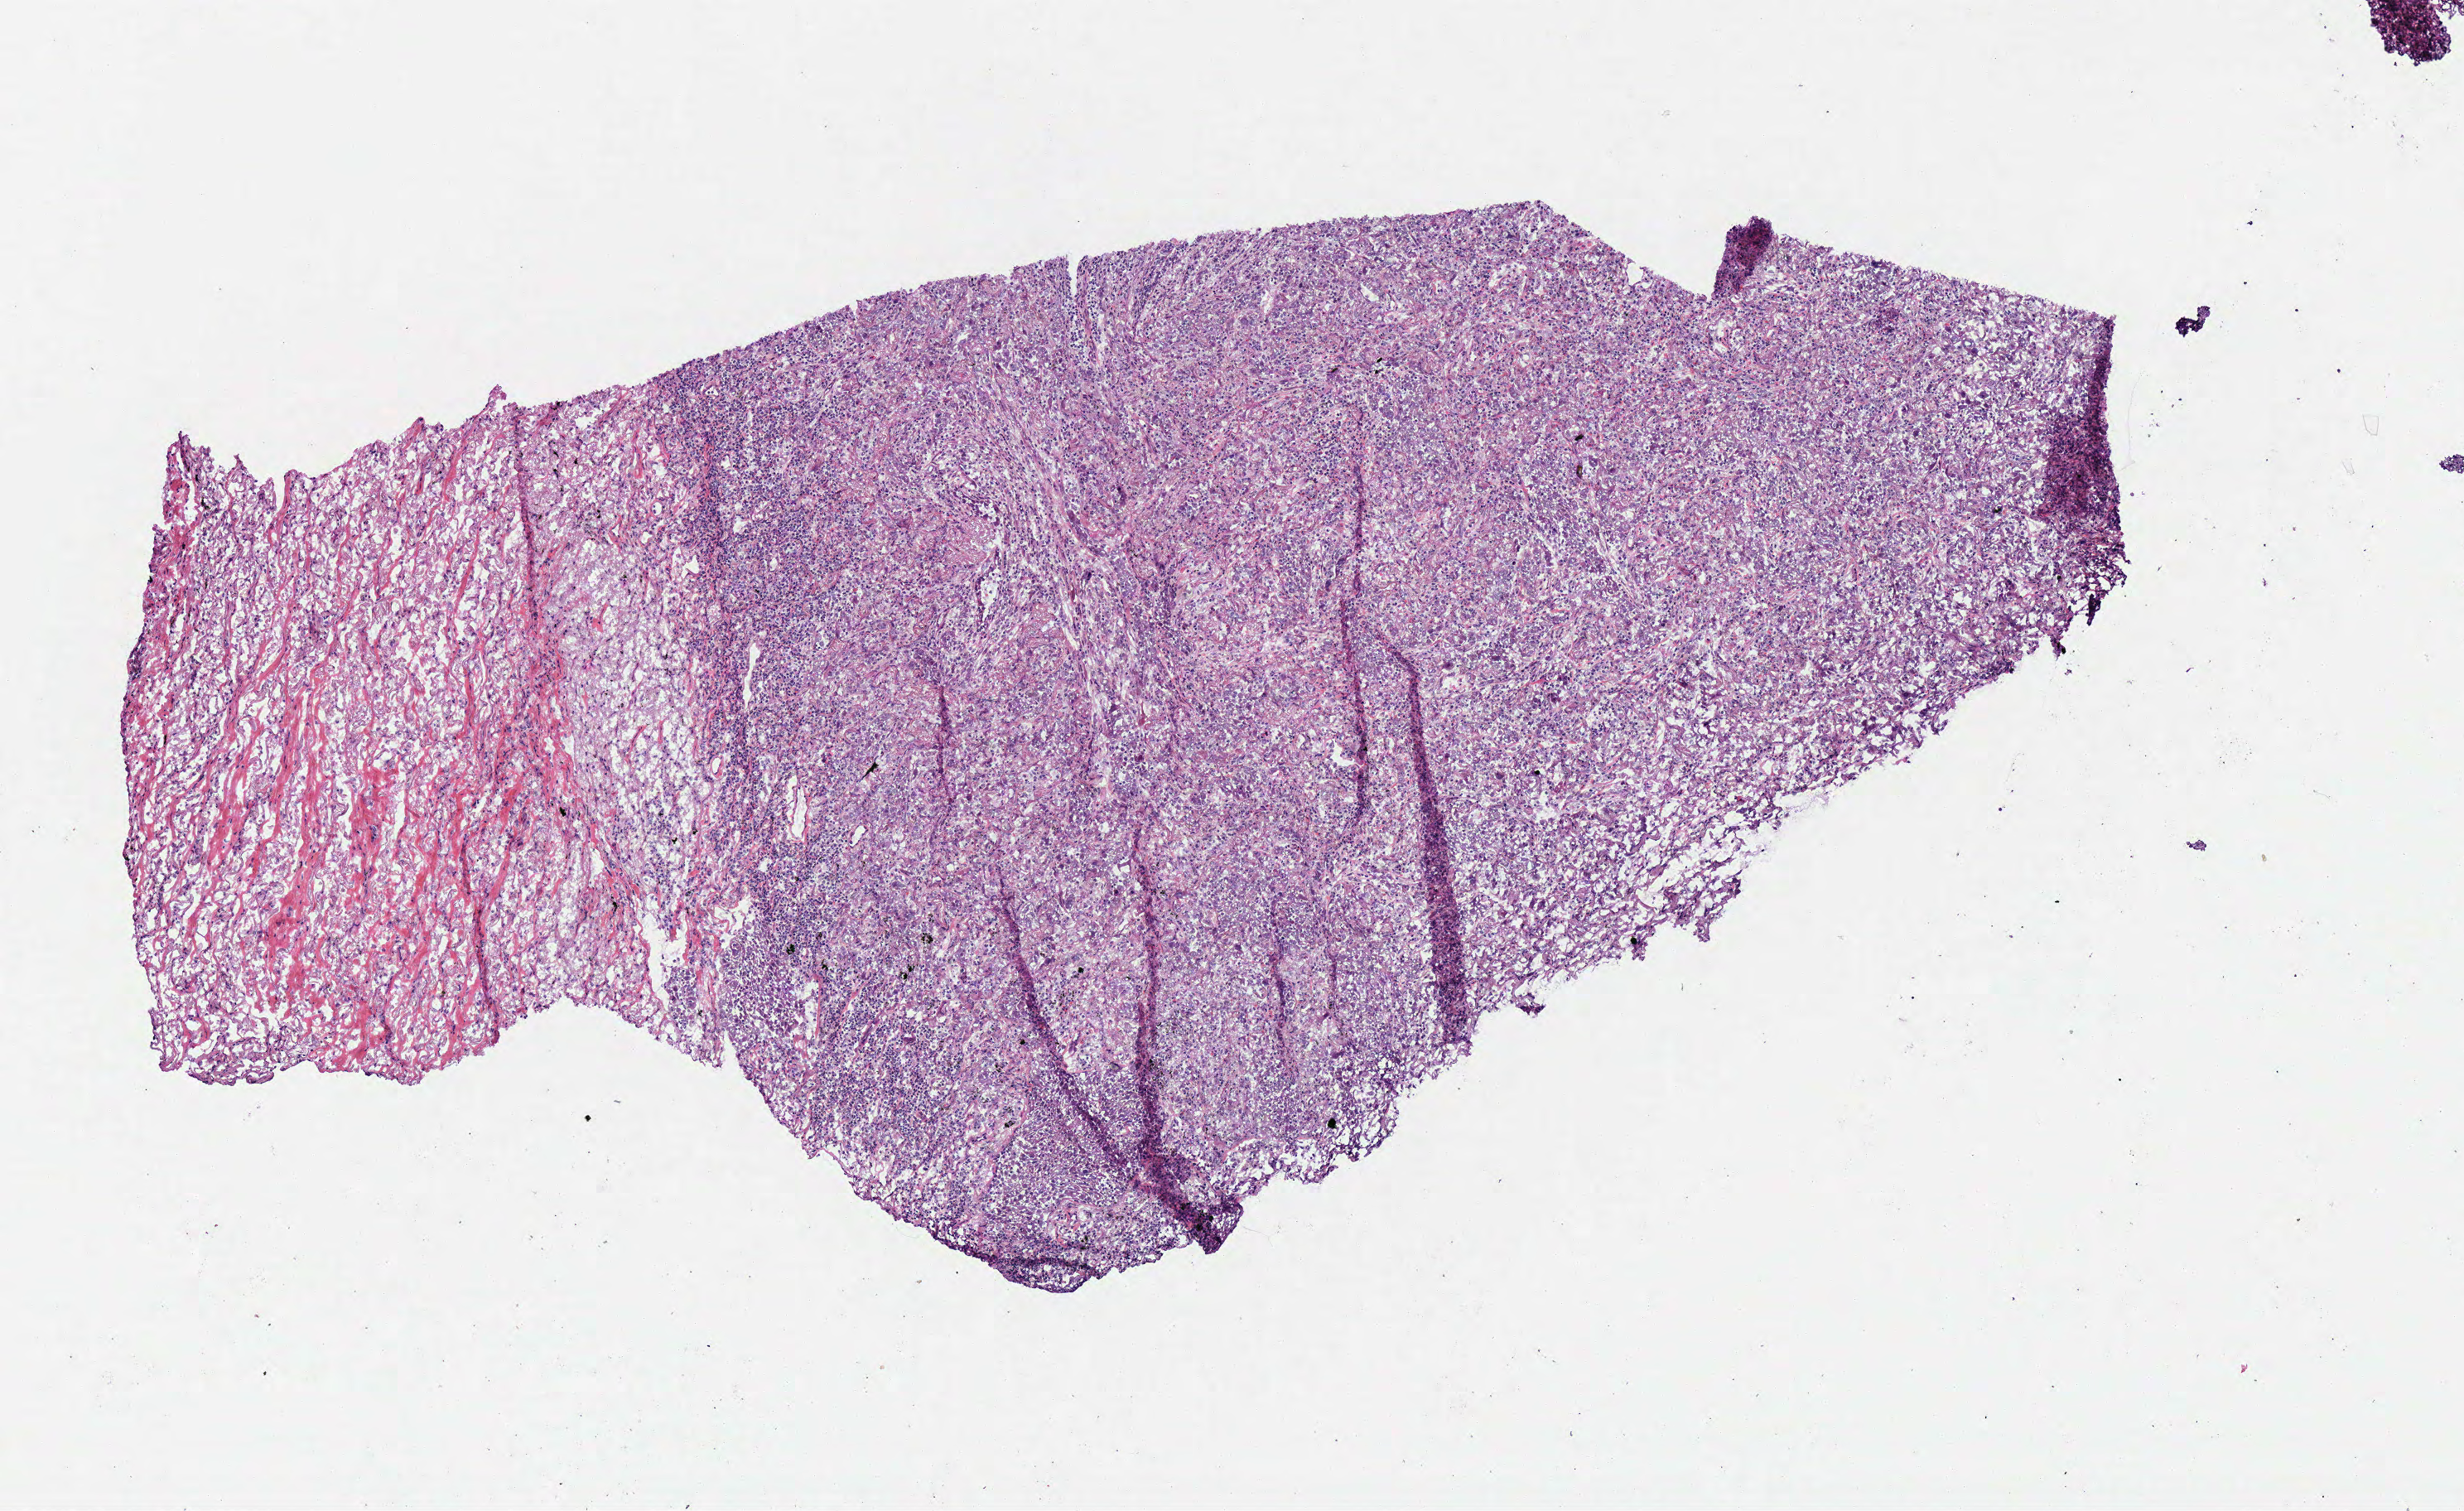
H&E-stained whole-slide image, shown as a low-resolution overview of the whole scanned area (about 5.9 x 3.6 mm, from a 40x scan), frozen section from the top of the tissue portion, sample: primary tumour, lung. Female patient. Composition of this section per pathologist review: tumour cells 70%, tumour nuclei 71%, normal cells 0%, stromal cells 30%, necrosis 0%. Inflammatory infiltration, as recorded: lymphocyte infiltration 20%, monocyte infiltration 2%, neutrophil infiltration 0%.
* laterality: left
* histologic diagnosis: Adenocarcinoma, NOS (upper lobe, lung)
* AJCC pathologic stage: IB
* TNM: T2a N0 M0